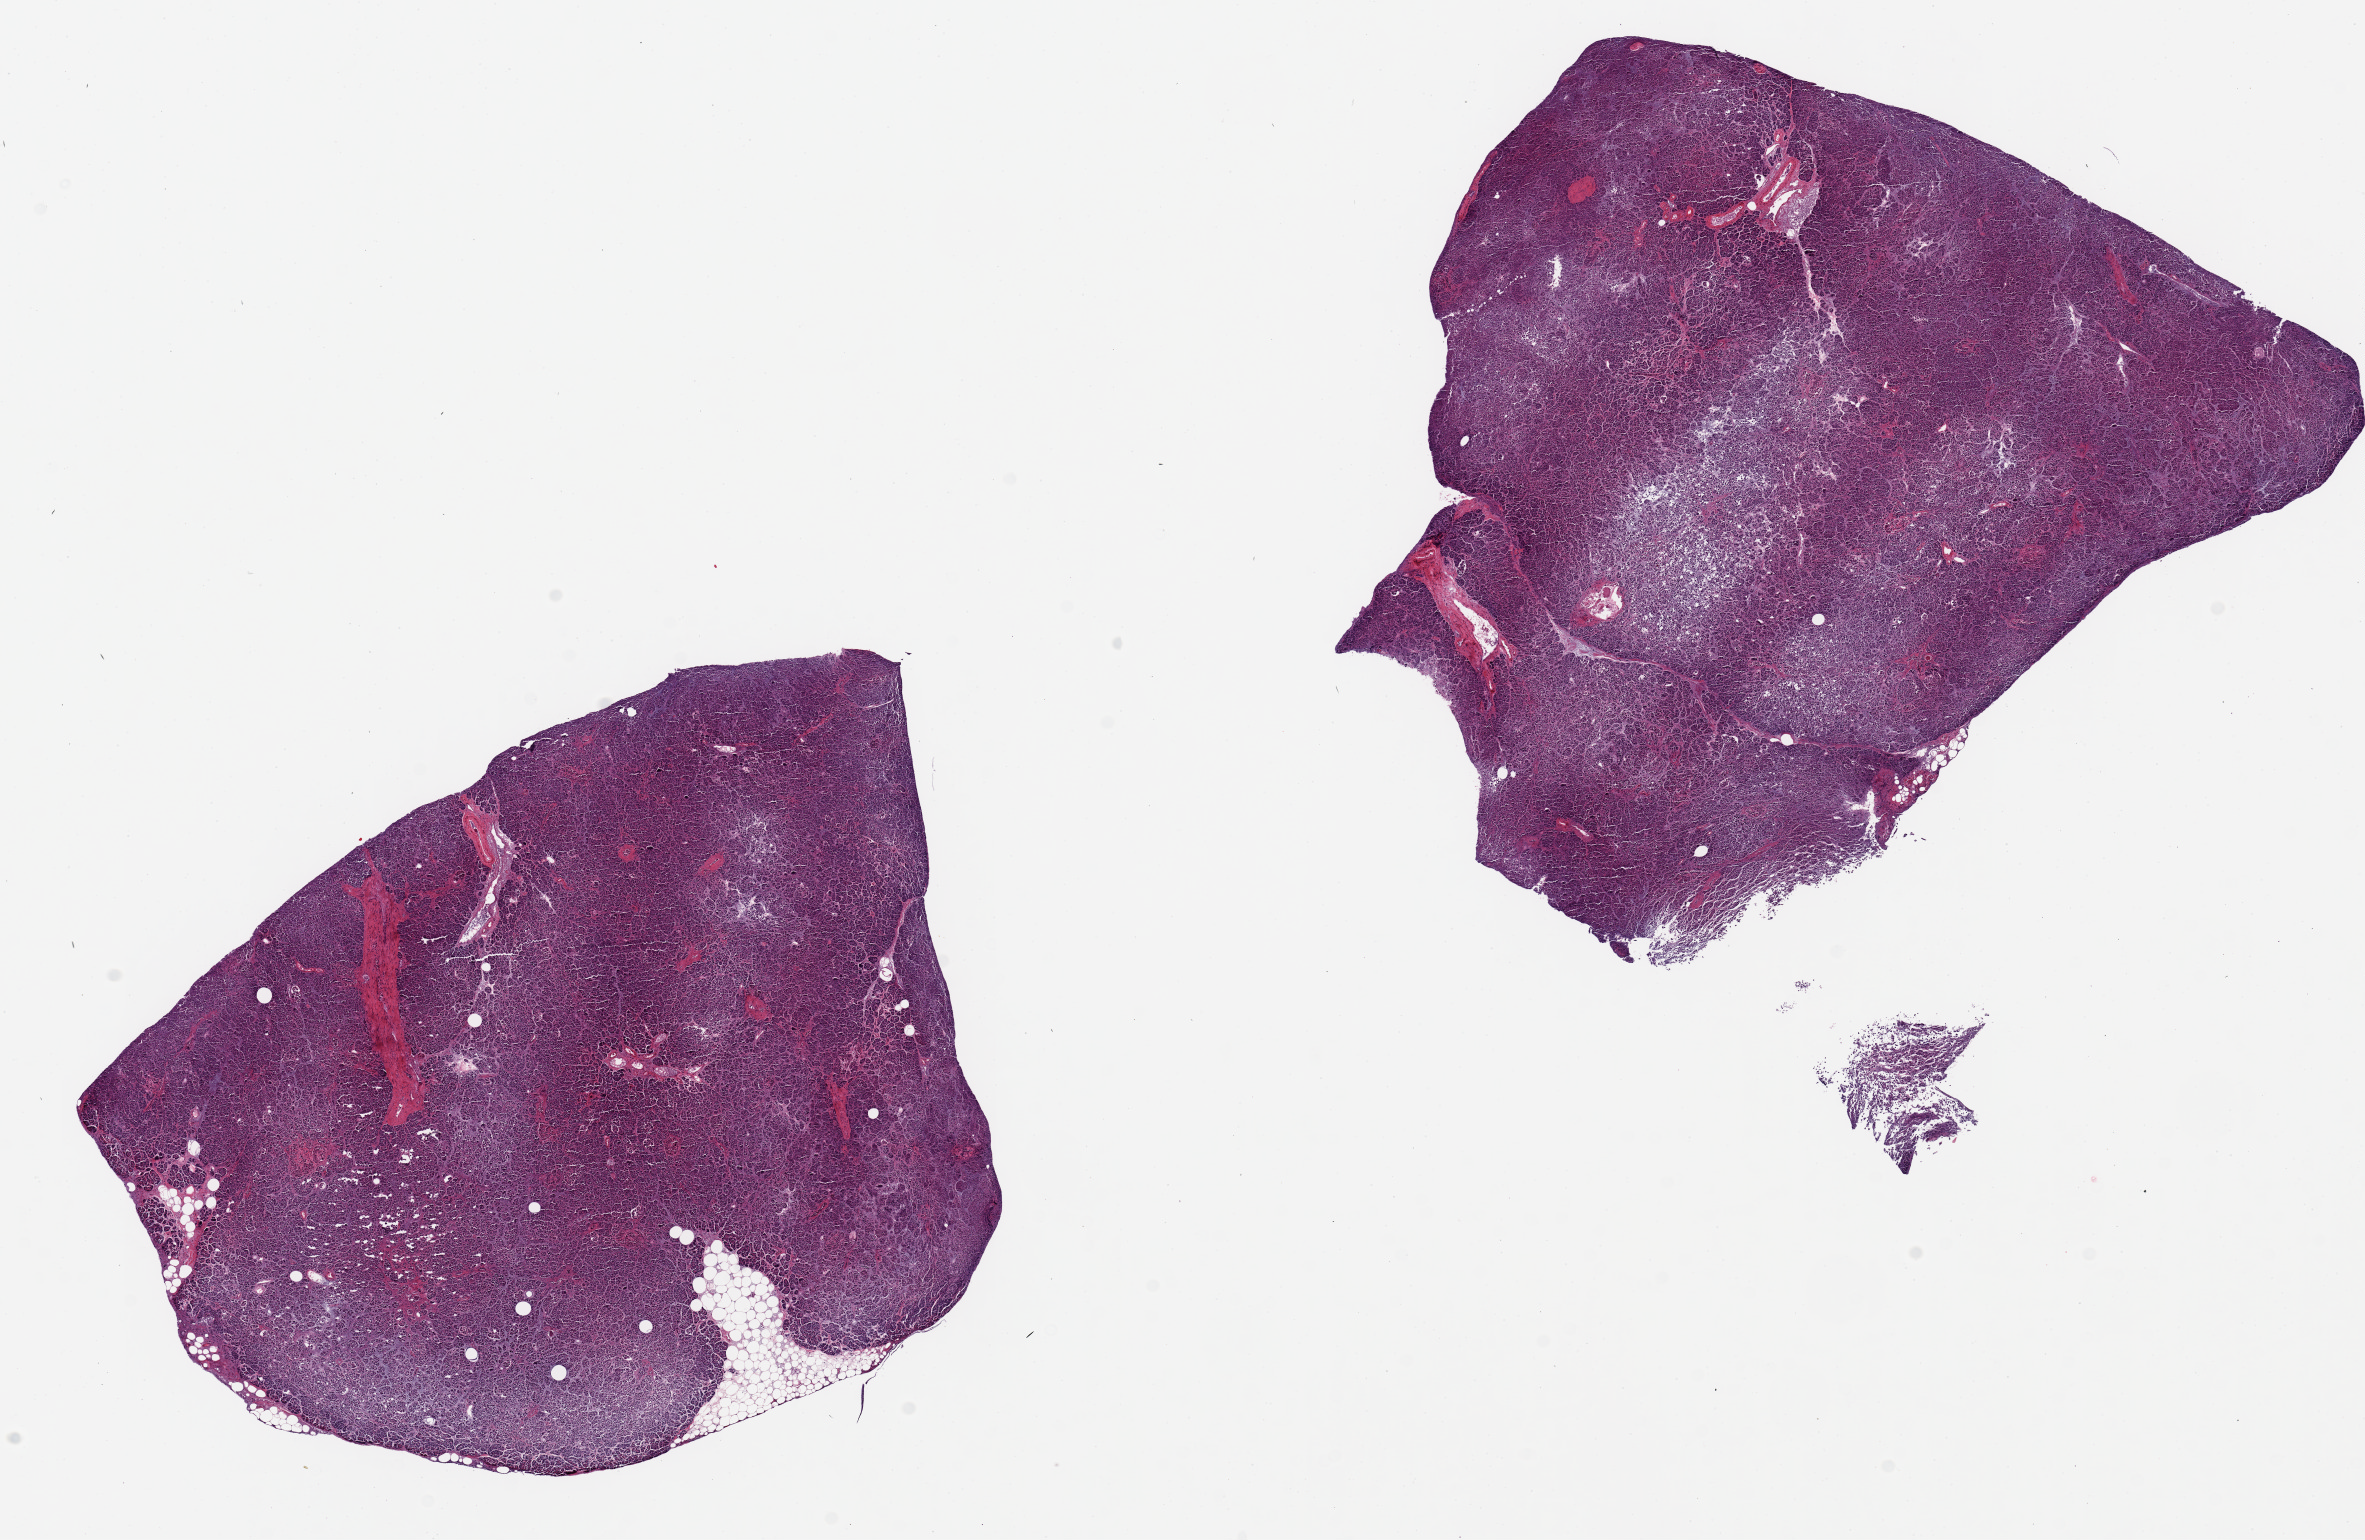
Digitized haematoxylin and eosin-stained section, whole scanned area (about 18.7 x 12.2 mm) shown as a low-resolution overview, PAXgene-fixed paraffin-embedded (PFPE) section, section of pancreas (target tissue), tissue donor sample. Donor sex: male.
* review note (as recorded): 2 pieces, 7x6 & 7x7mm